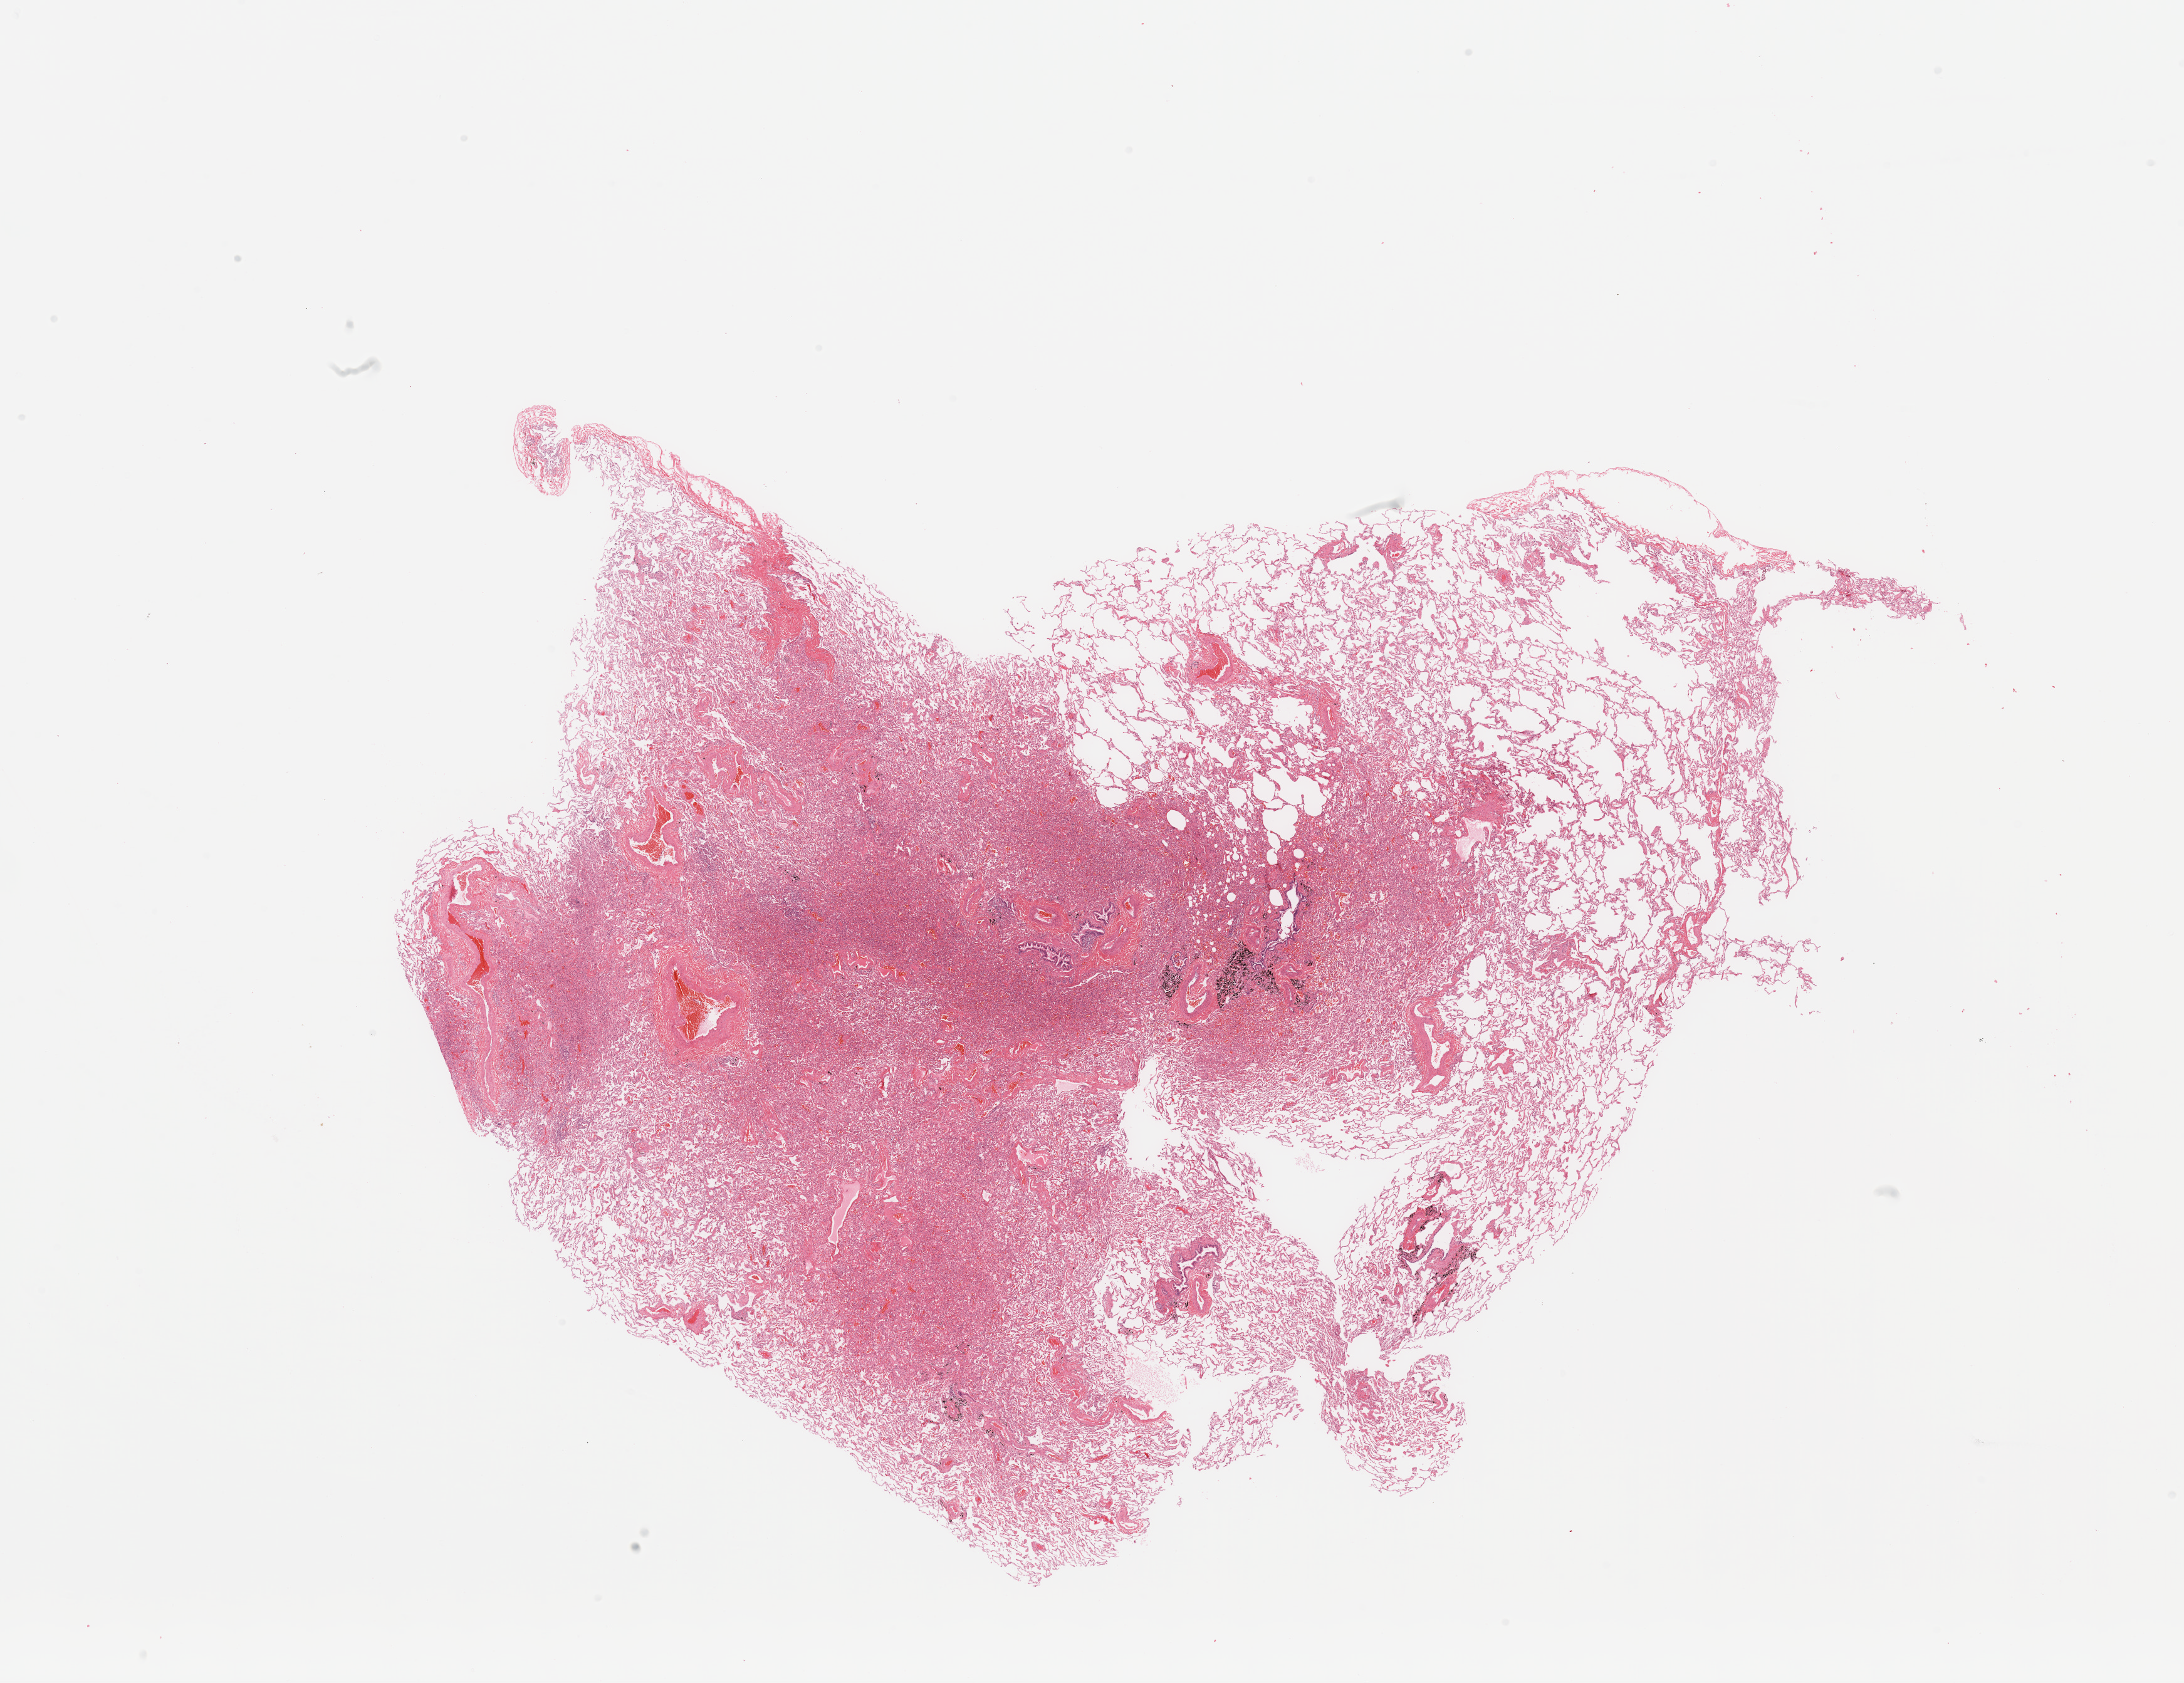
H&E whole-slide image, a low-resolution overview of the entire scanned area, about 27.6 x 21.2 mm (slide scanned at 20x), normal (non-tumour) tissue sample, lung. Patient: female, age 48 years.
This section: normal (non-tumour) tissue from the same patient. Patient diagnosis: Adenocarcinoma, NOS.